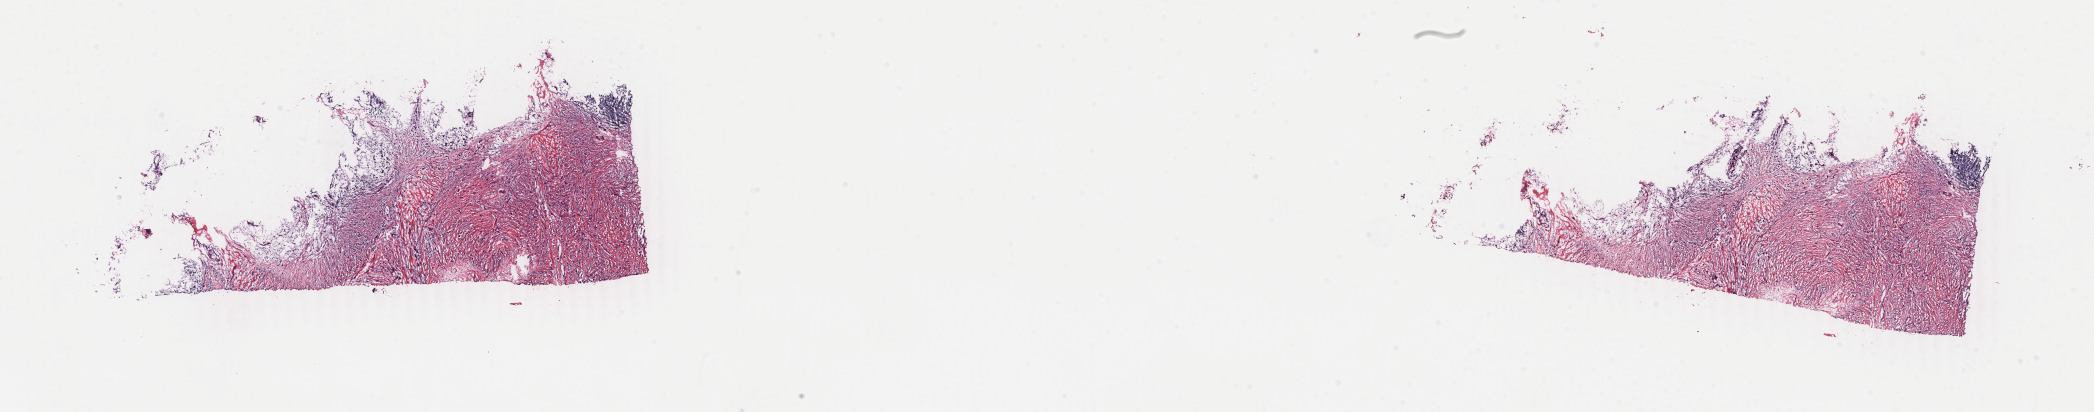
Digitized H&E-stained tissue section (whole slide), a low-resolution overview of the entire scanned area, about 33.3 x 6.6 mm (slide scanned at 40x); frozen section from the top of the tissue portion; breast, primary tumour sample. Patient: female, age at initial diagnosis 50 years. Pathologist review of this section (percent, as recorded): tumour cells 75%, tumour nuclei 75%, normal cells 0%, stromal cells 25%, necrosis 0%. Inflammatory infiltration, as recorded: lymphocyte infiltration 20%, monocyte infiltration 10%, neutrophil infiltration 10%.
Lymph nodes positive (case pathology): 0 of 3 examined. Diagnosis: Lobular carcinoma, NOS. AJCC pathologic stage: IIB.